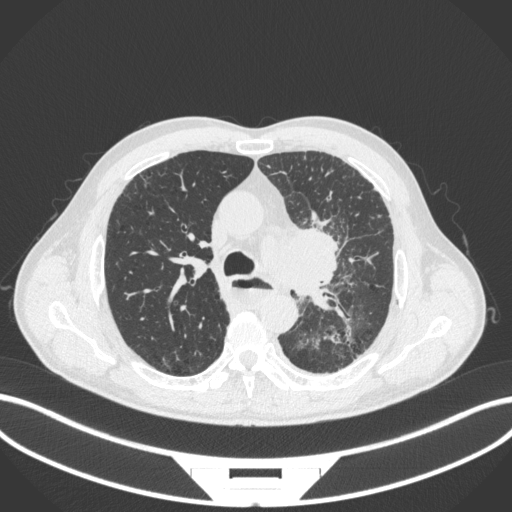
Chest CT, one axial slice; position 259 of 411 along the scan axis; lung window (W 1500 / L -600 HU); 1 mm slice thickness; 512 × 512 image matrix, field of view 400 × 400 mm. Patient: male, 57 years. From the clinical record (not read from this slice): clinical TNM (as recorded): T2a N1 M0.
Outlined on this slice (rectangle marked by the reading radiologist):
- lung tumour (recorded histology: squamous cell carcinoma): bounding box <263,216,358,310> (left, top, right, bottom; pixels)